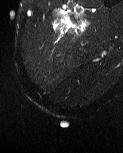
MRI of an extremity soft-tissue mass, one axial slice; position 6 of 60 along the scan axis; T2-weighted fat-saturated; MR volume resampled by the dataset authors to the PET/CT grid (not the native acquisition matrix); 123 × 153 image matrix, field of view 120 × 149 mm. Male patient. Case-level facts recorded for this patient, not image findings: histological type: pleiomorphic liposarcoma; grade: high; site of the primary tumour: left thigh.
Outlined on this slice (expert contour drawn on MRI and transferred to this co-registered scan by the dataset authors):
- gross tumour volume including surrounding oedema: bounding box <54,15,89,35> (left, top, right, bottom; pixels)